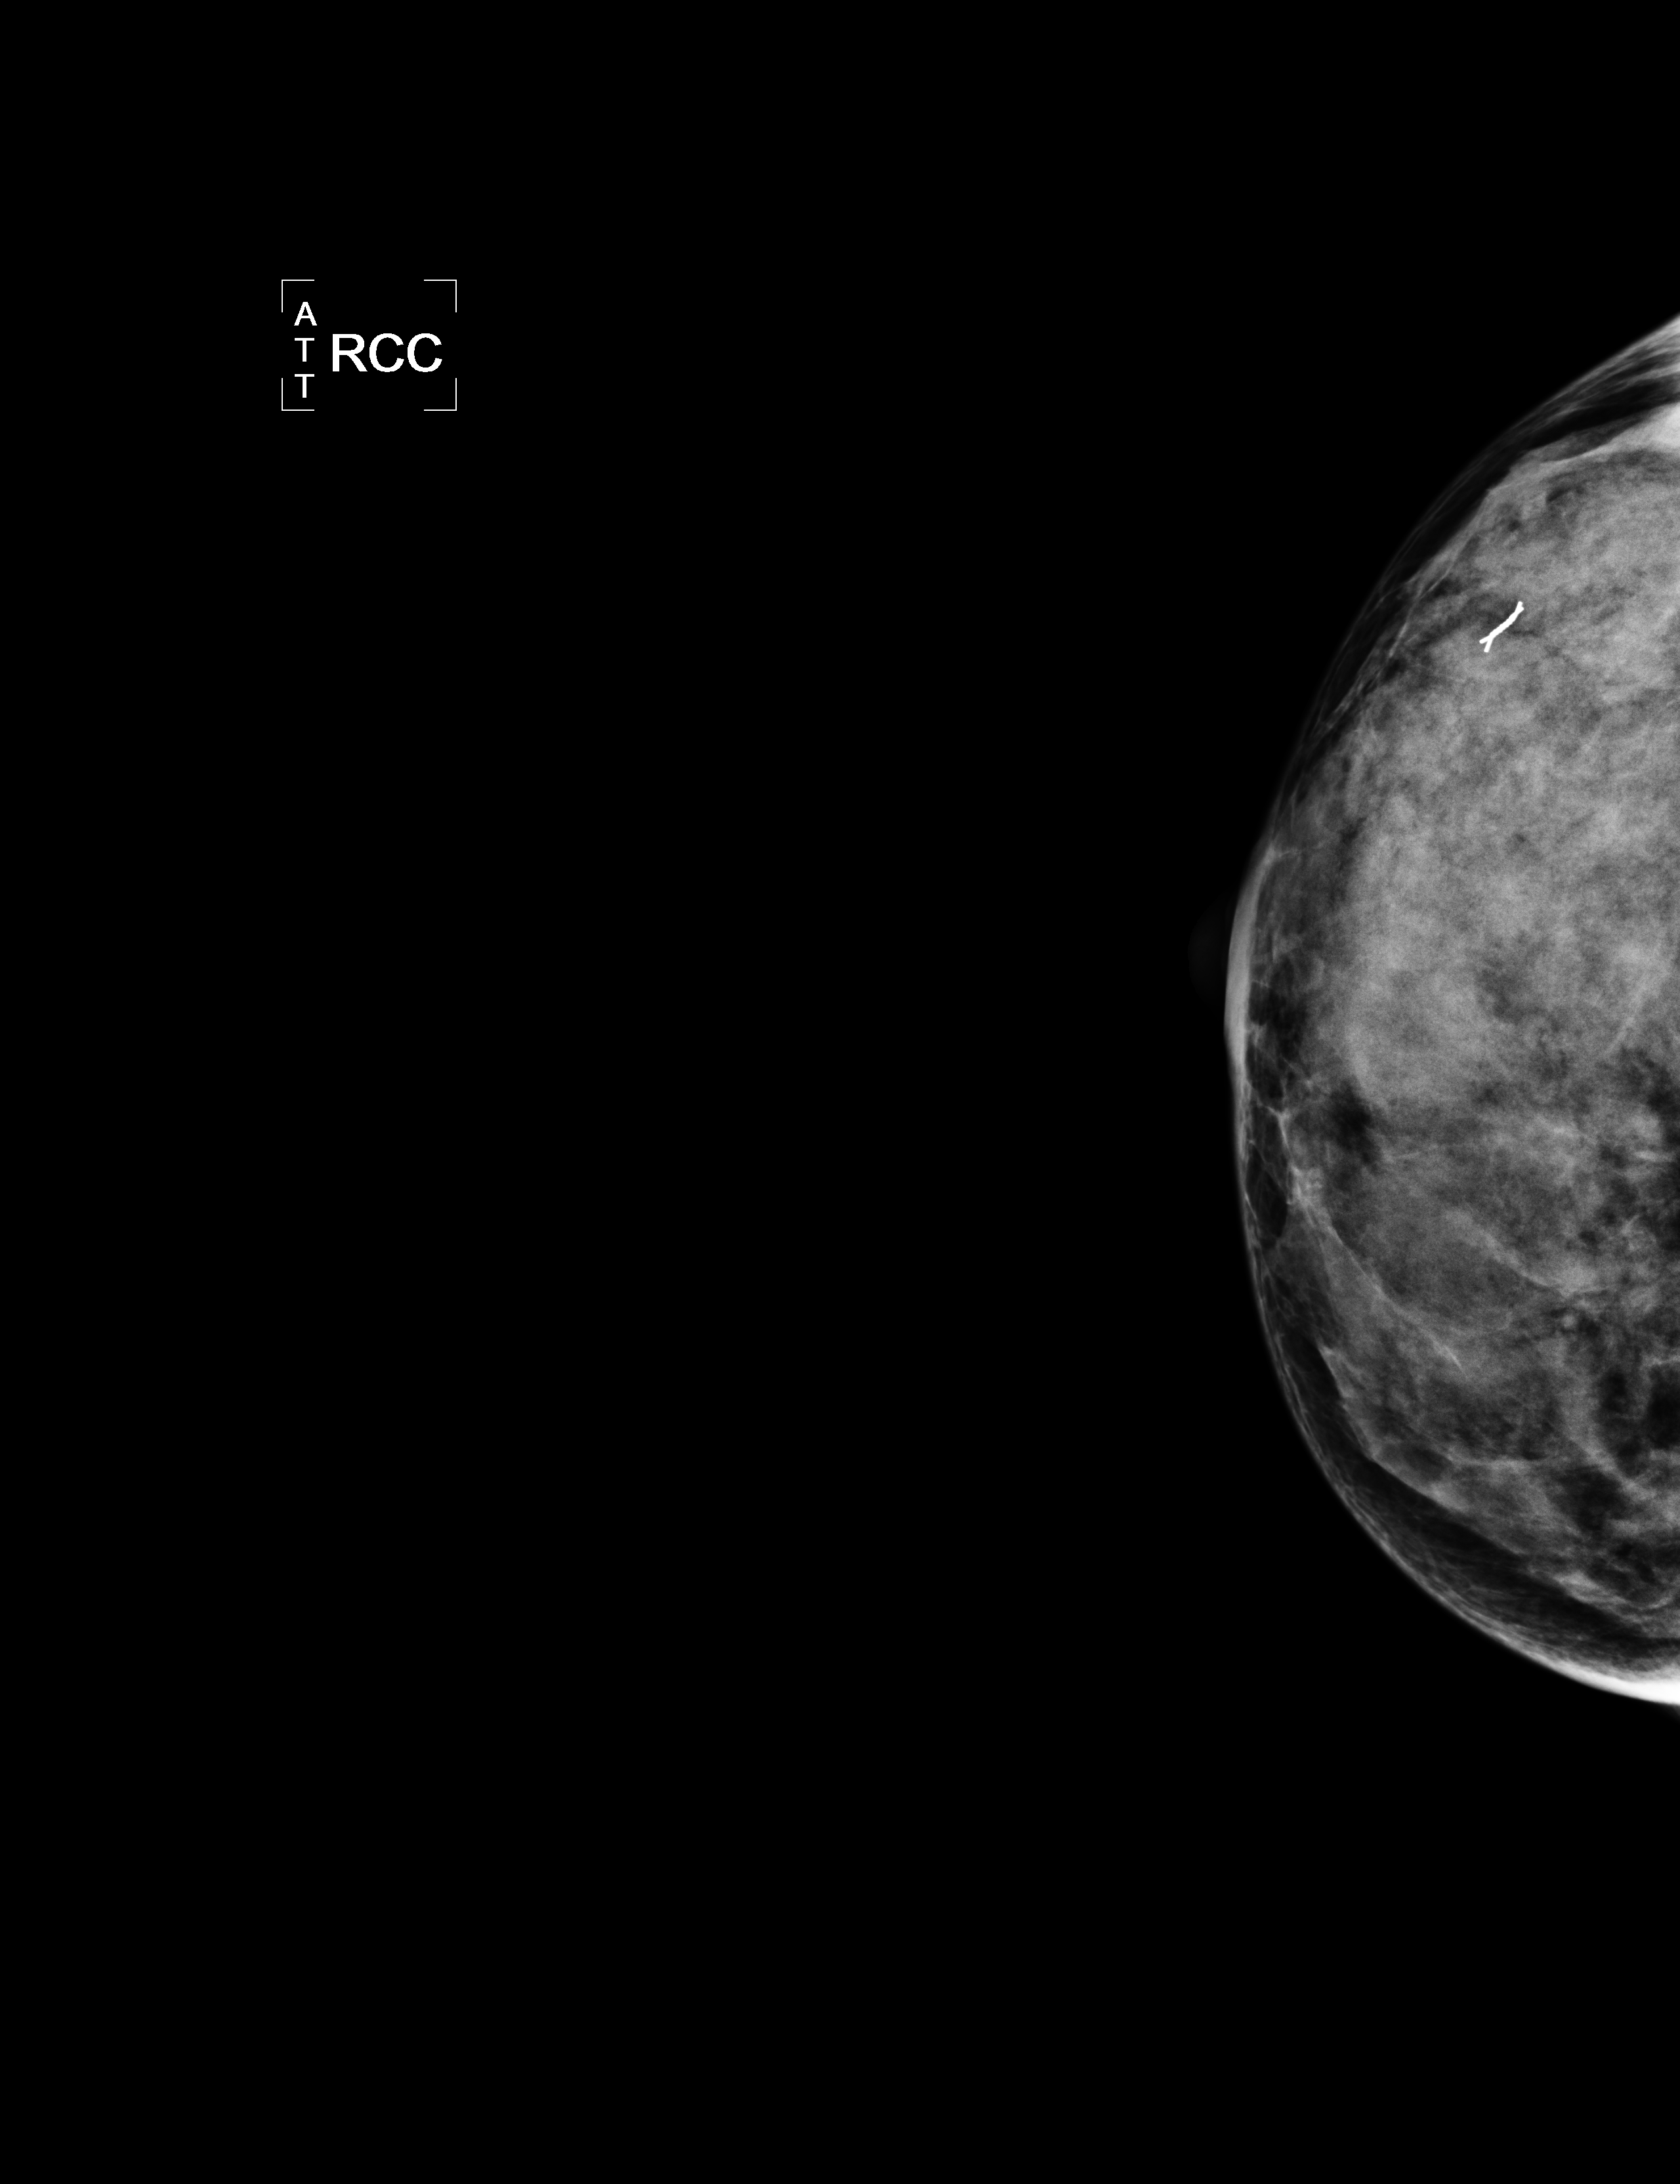
Mammogram, right breast, CC view.
Pathology recorded for this patient (not read from this image): pathology diagnosis: Invasive ductal carcinoma, modified Scarff-Bloom-Richardson grade II/III. No intraductal carcinoma component seen. (right breast); receptor status (as recorded): ER pos (strong), PR pos (strong), HER2 neg (weak); Ki-67 (as recorded): pos (strong).